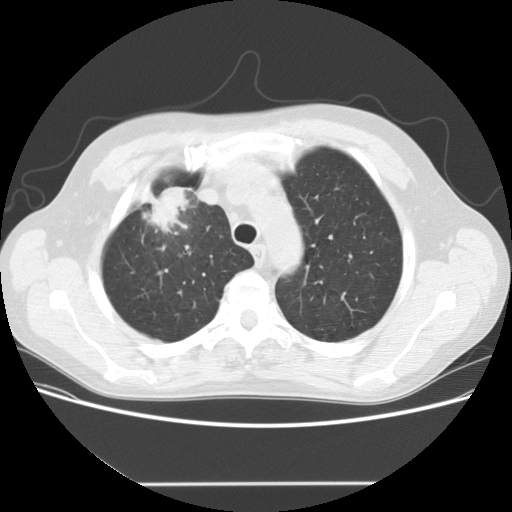
Chest CT (low-dose screening protocol), one axial image, baseline annual screen, lung window (W 1500 / L -600 HU), standard (soft-tissue) reconstruction kernel (STANDARD), slice 31 of 153 in the series, 512 × 512 image matrix, field of view 360 × 360 mm. Male participant, aged 56 years at enrolment. Current smoker at enrolment.
- Expert reader's lesion annotation, box from (x=128, y=175) to (x=208, y=241) px.
- The screening reader recorded 2 non-calcified nodules or masses ≥4 mm on this exam (right upper lobe, right middle lobe); which of them this box marks is not recorded.
- Official screen result: positive, change unspecified: nodule(s) >= 4 mm or enlarging nodule(s), mass(es), or other non-specific abnormalities suspicious for lung cancer.
- Participant outcome: lung cancer diagnosed 120 days after this screen — adenocarcinoma, NOS, right upper lobe, stage IIIA (AJCC 6th edition), 34 mm at pathology.